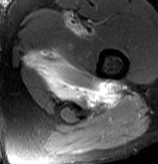
MRI of an extremity soft-tissue mass, one axial slice. Position 68 of 70 along the scan axis. T2-weighted fat-saturated. MR volume resampled by the dataset authors to the PET/CT grid (not the native acquisition matrix). 158 × 164 image matrix, field of view 154 × 160 mm. Male patient. From the clinical record (not read from this slice): histological type: extraskeletal osteosarcoma; grade: high; site of the primary tumour: left adductur.
Annotated regions visible in this slice (expert contour drawn on MRI and transferred to this co-registered scan by the dataset authors):
- gross tumour volume (mass): box from (x=24, y=11) to (x=126, y=109) px